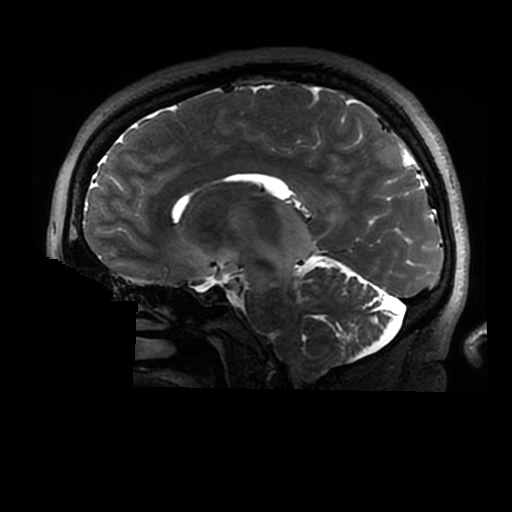
Brain MRI from a brain-tumour surgery series, one sagittal slice; slice 169 of 320 in the series (ordered by position); 0.6 mm slice thickness; 512 × 512 image matrix, field of view 240 × 240 mm. Case-level facts recorded for this patient, not image findings: histopathology: Astrocytoma; WHO grade: 2; IDH mutation: yes.
Annotated regions visible in this slice (outlined manually by an expert reader):
- tumour: bounding box <204,202,315,279> (left, top, right, bottom; pixels)